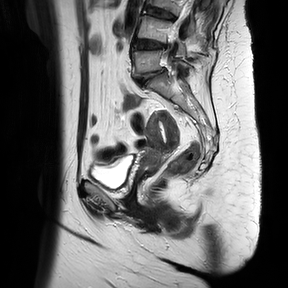
Pelvic MRI for cervical cancer, one sagittal slice; slice 22 of 37 in the series (ordered by position); T2-weighted; 1.5 T; TE 100 ms, TR 4174.1 ms; 4 mm slice thickness; 288 × 288 image matrix, field of view 300 × 300 mm. Female patient, age 65 years.
Structures marked on this image (outlined manually by an expert reader):
- uterus and cervix: bounding box <136,108,180,182> (left, top, right, bottom; pixels)